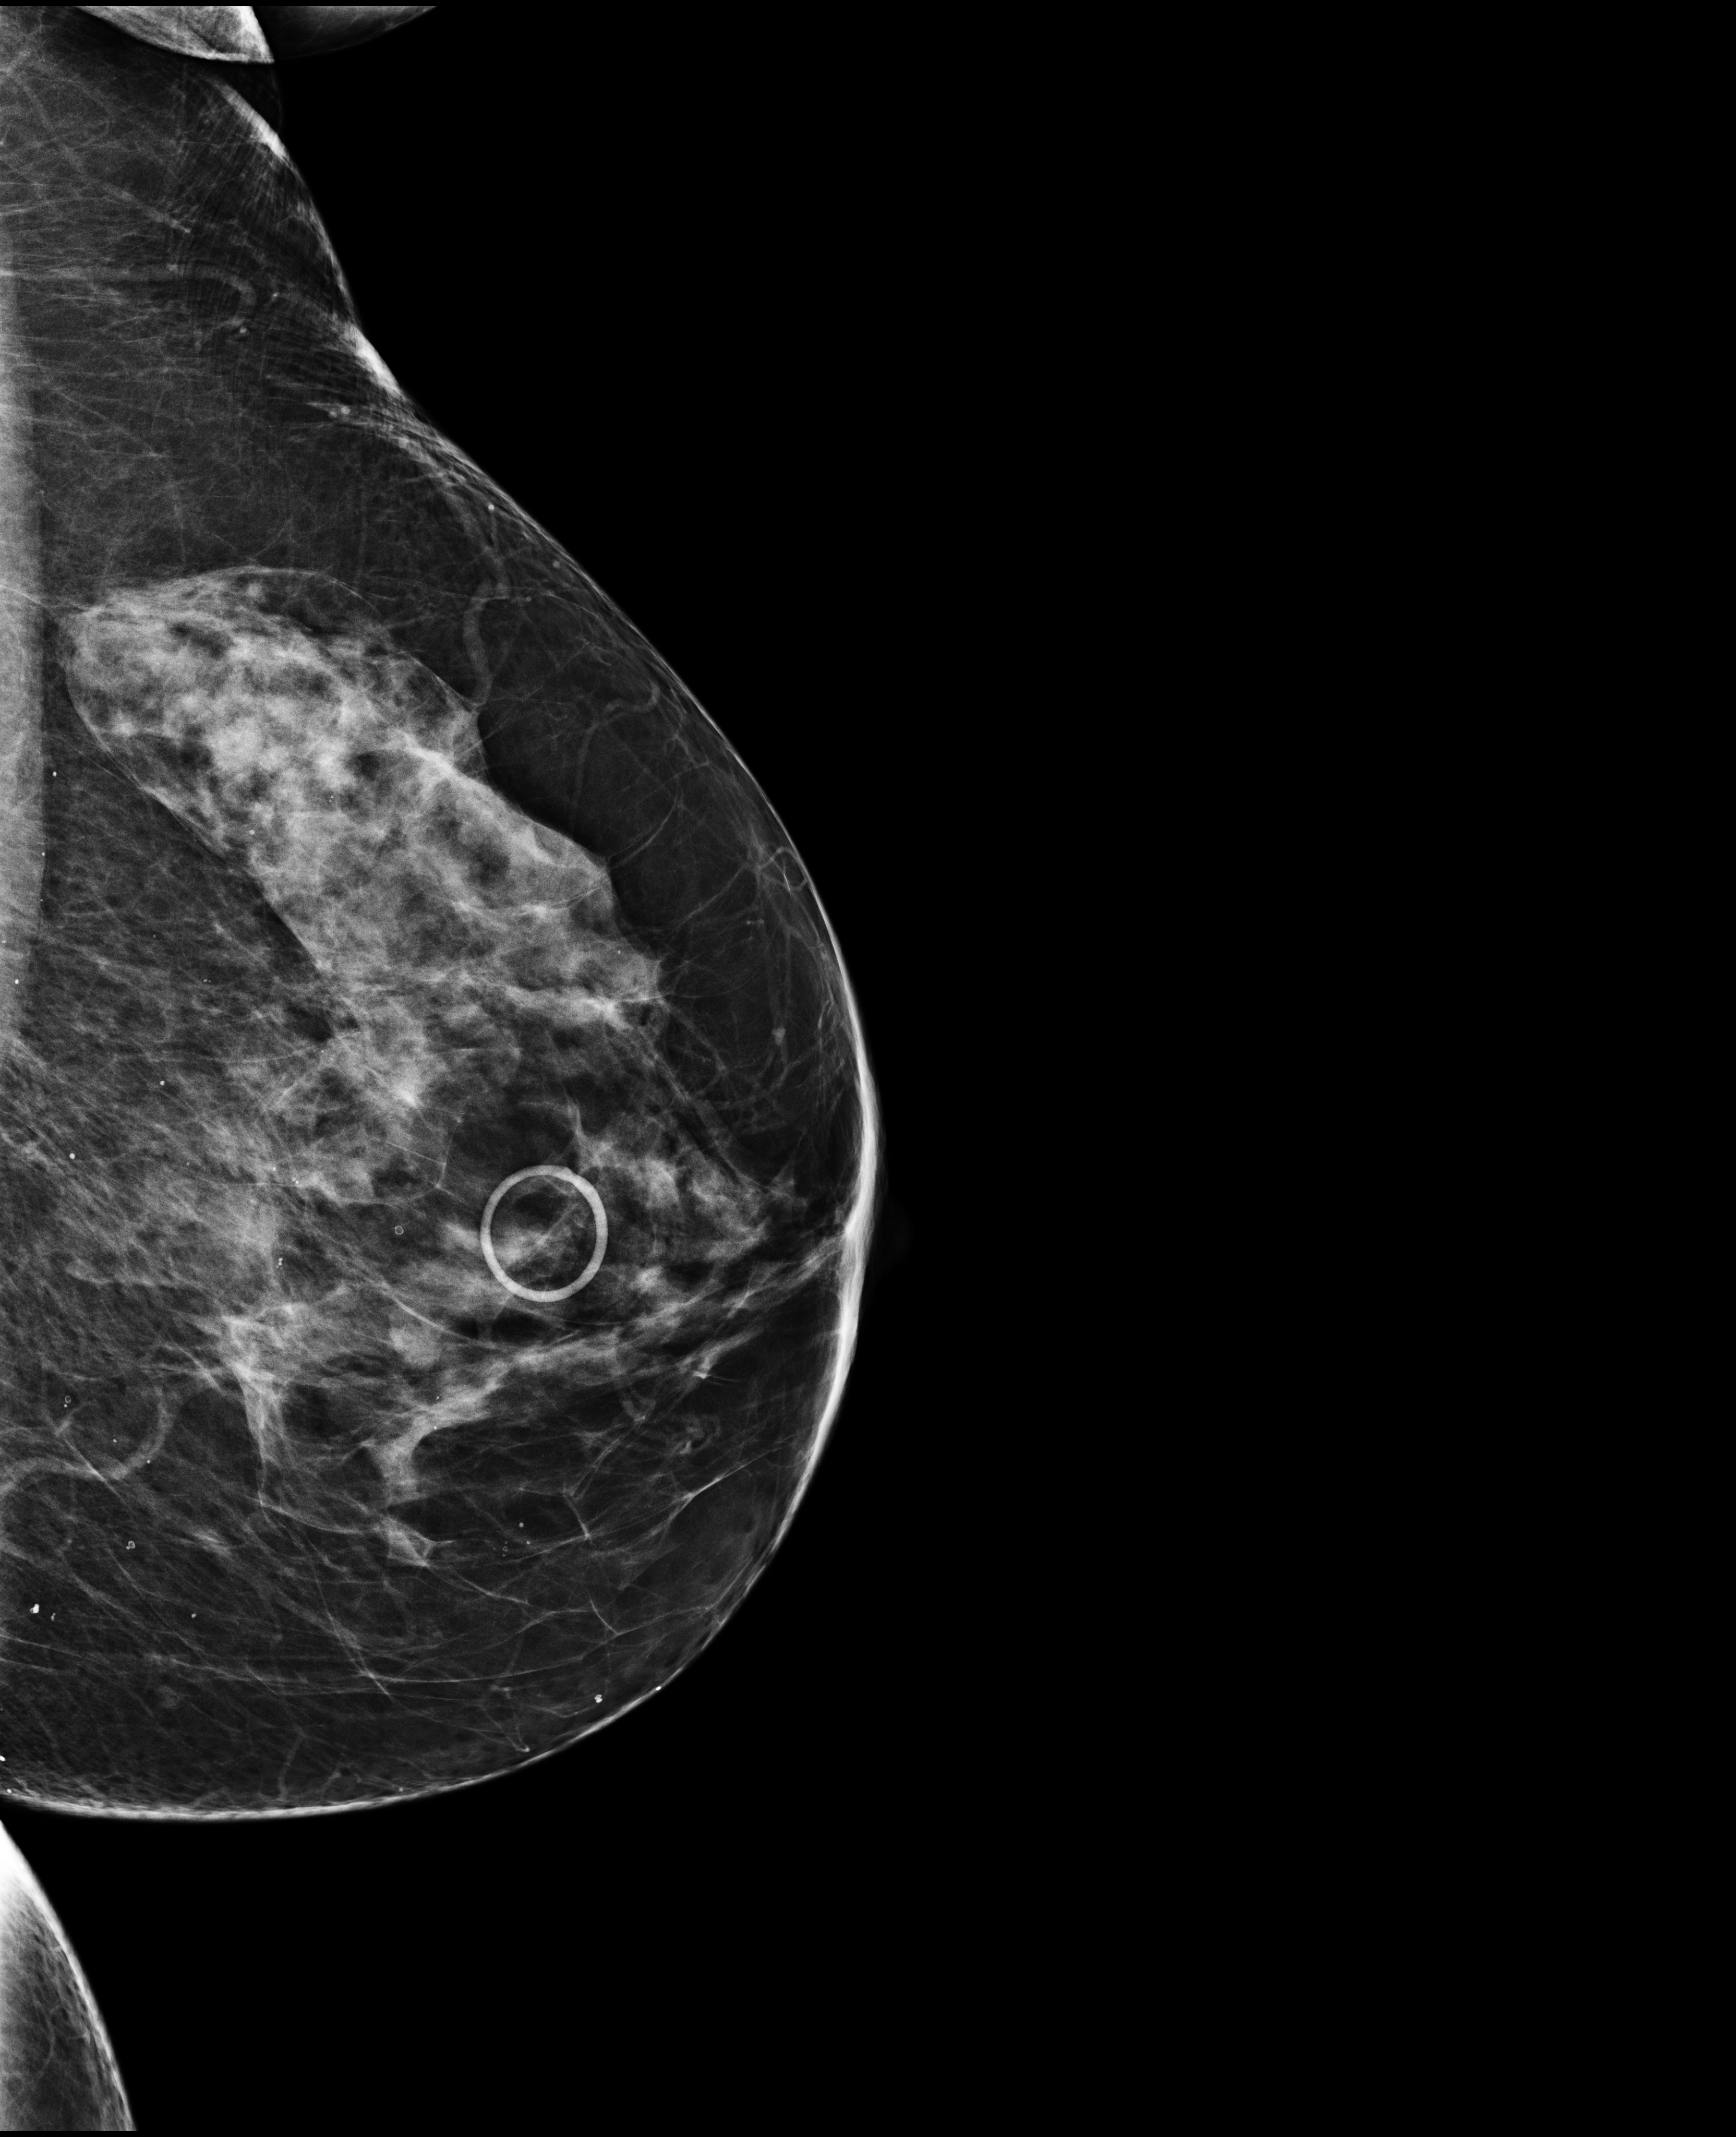
Full-field digital mammogram (FFDM), left breast, exaggerated CC view (lateral), screening examination. Patient: female, 60 years.
BI-RADS breast density category at the screening exam (both breasts, scale 1–4): 3. Final BI-RADS assessment for this screening round (tomosynthesis exam, both breasts): category 1. Recall: recalled for additional imaging after this screen.